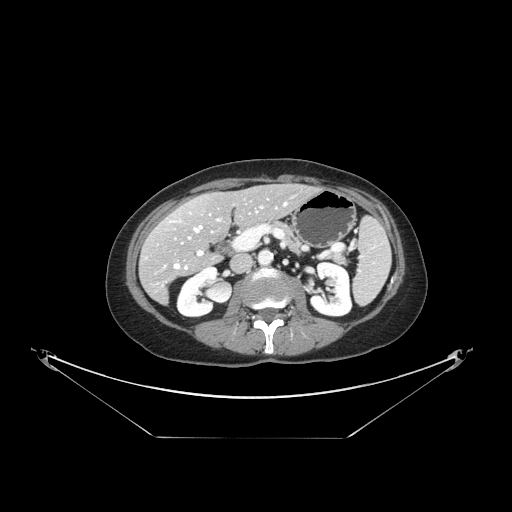
Contrast-enhanced abdominal CT, one axial slice. Slice 70 of 148 in the series (ordered by position). Reconstruction kernel STANDARD. 120 kVp. Intravenous contrast given. Soft-tissue window (W 400 / L 40 HU). 2.5 mm slice thickness. 512 × 512 image matrix, field of view 500 × 500 mm. Female patient, age 73 years. Case-level facts recorded for this patient, not image findings: diagnosis: colorectal cancer liver metastases, imaged before liver resection; multiple liver metastases: no; largest metastasis: 1 cm; chemotherapy before resection: yes.
Outlined on this slice (outlined manually by an expert reader):
- hepatic veins: bounding box <171,203,287,269> (left, top, right, bottom; pixels)
- liver: <141,185,314,301>
- planned liver remnant (the part of the liver to remain after resection): <168,186,314,247>
- portal vein (with intrahepatic branches): <198,207,262,256>